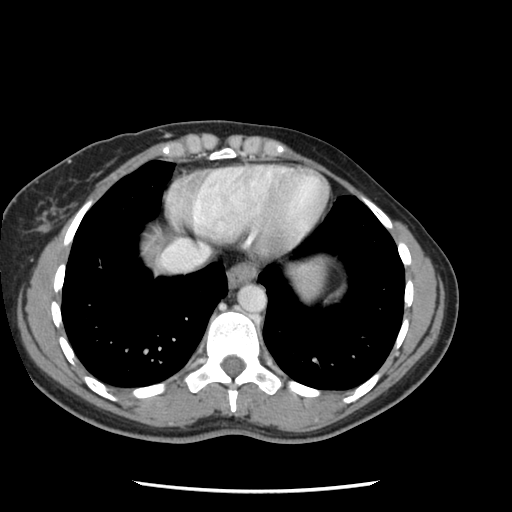
Contrast-enhanced abdominal CT, one axial slice. Position 114 of 134 along the scan axis. 120 kVp. Intravenous contrast given. Soft-tissue window (W 400 / L 40 HU). 2.5 mm slice thickness. 512 × 512 image matrix, field of view 330 × 330 mm. Female patient, age 43 years. From the clinical record (not read from this slice): diagnosis: colorectal cancer liver metastases, imaged before liver resection; multiple liver metastases: yes; largest metastasis: 3.4 cm.
Structures marked on this image (outlined manually by an expert reader):
- hepatic veins: bounding box <163,241,208,268> (left, top, right, bottom; pixels)